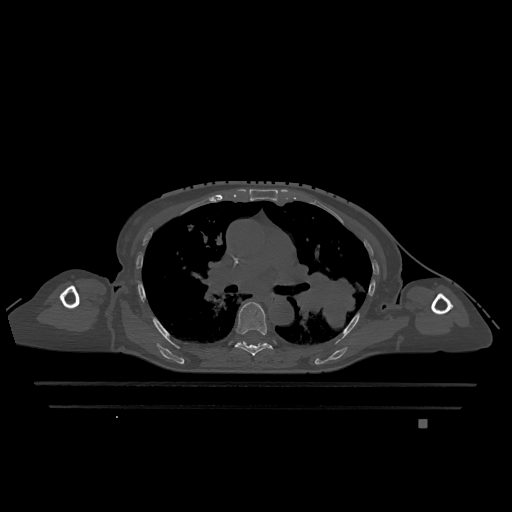
CT including the spine, one axial slice; slice 785 of 1317 in the series (ordered by position); bone window (W 1800 / L 400 HU); 0.5 mm slice thickness; 512 × 512 image matrix, field of view 500 × 500 mm. Female patient, age 74 years. From the clinical record (not read from this slice): primary cancer: lung; vertebrae with lytic lesions (as recorded): T1, T4, T5, T6, L4, L5.
Annotated regions visible in this slice (semi-automatically segmented with operator editing):
- T6 vertebra: bounding box <235,302,273,356> (left, top, right, bottom; pixels)